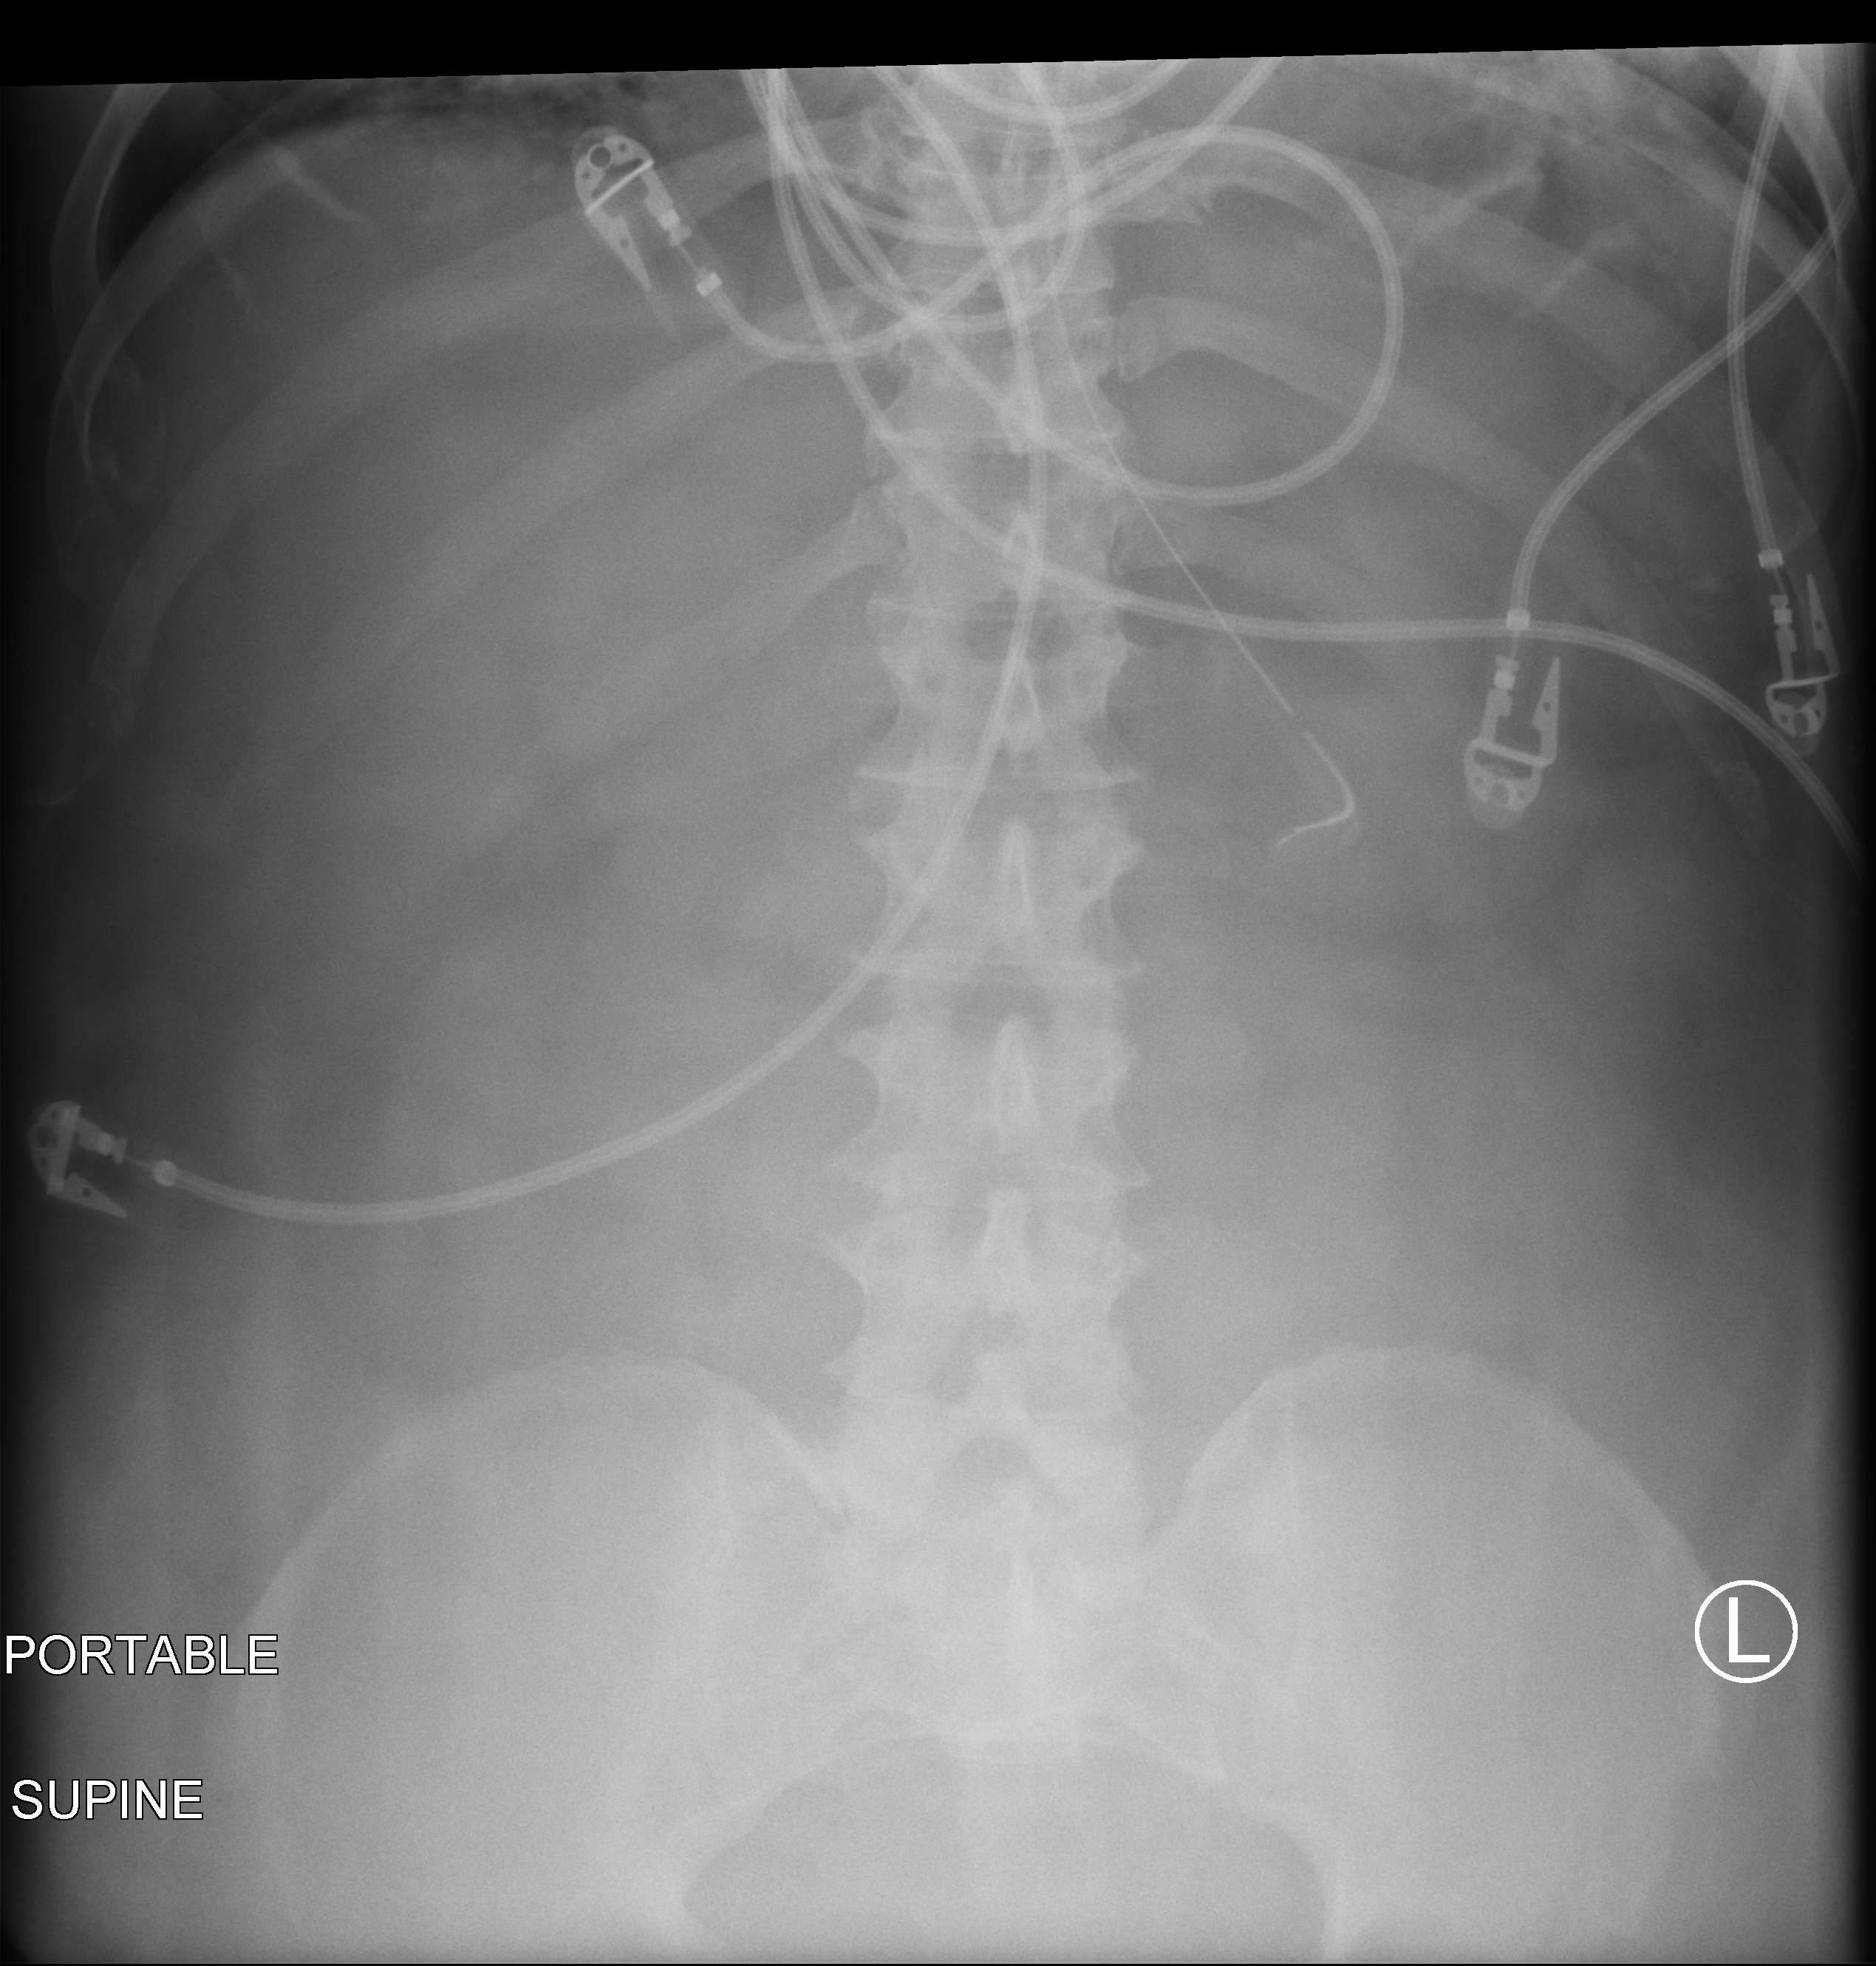
Portable abdomen radiograph, anteroposterior (AP) projection. Male patient hospitalised with COVID-19, age 60–74 years.
From the hospital-stay record, not from the radiograph (when in the stay this image was taken is not recorded):
- admitted to intensive care during this hospital stay: yes
- length of hospital stay: 28 days
- mechanically ventilated during this hospital stay: yes